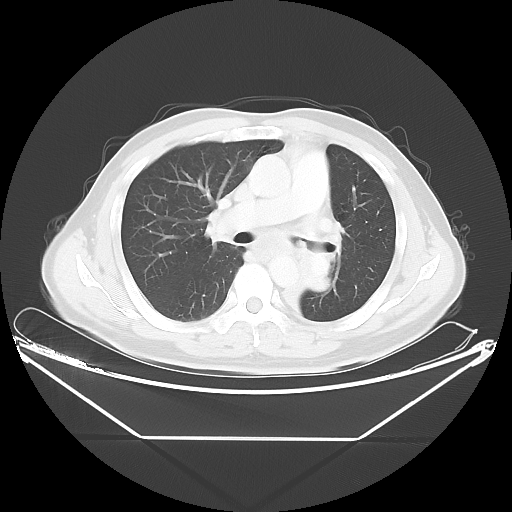
Chest CT, one axial slice; position 28 of 48 along the scan axis; lung window (W 1500 / L -600 HU); 5 mm slice thickness; 512 × 512 image matrix. Patient: male, 58 years. From the clinical record (not read from this slice): clinical TNM (as recorded): T3 N3 M0.
Annotated regions visible in this slice (rectangle marked by the reading radiologist):
- lung tumour (recorded histology: squamous cell carcinoma): bounding box <284,239,343,333> (left, top, right, bottom; pixels)